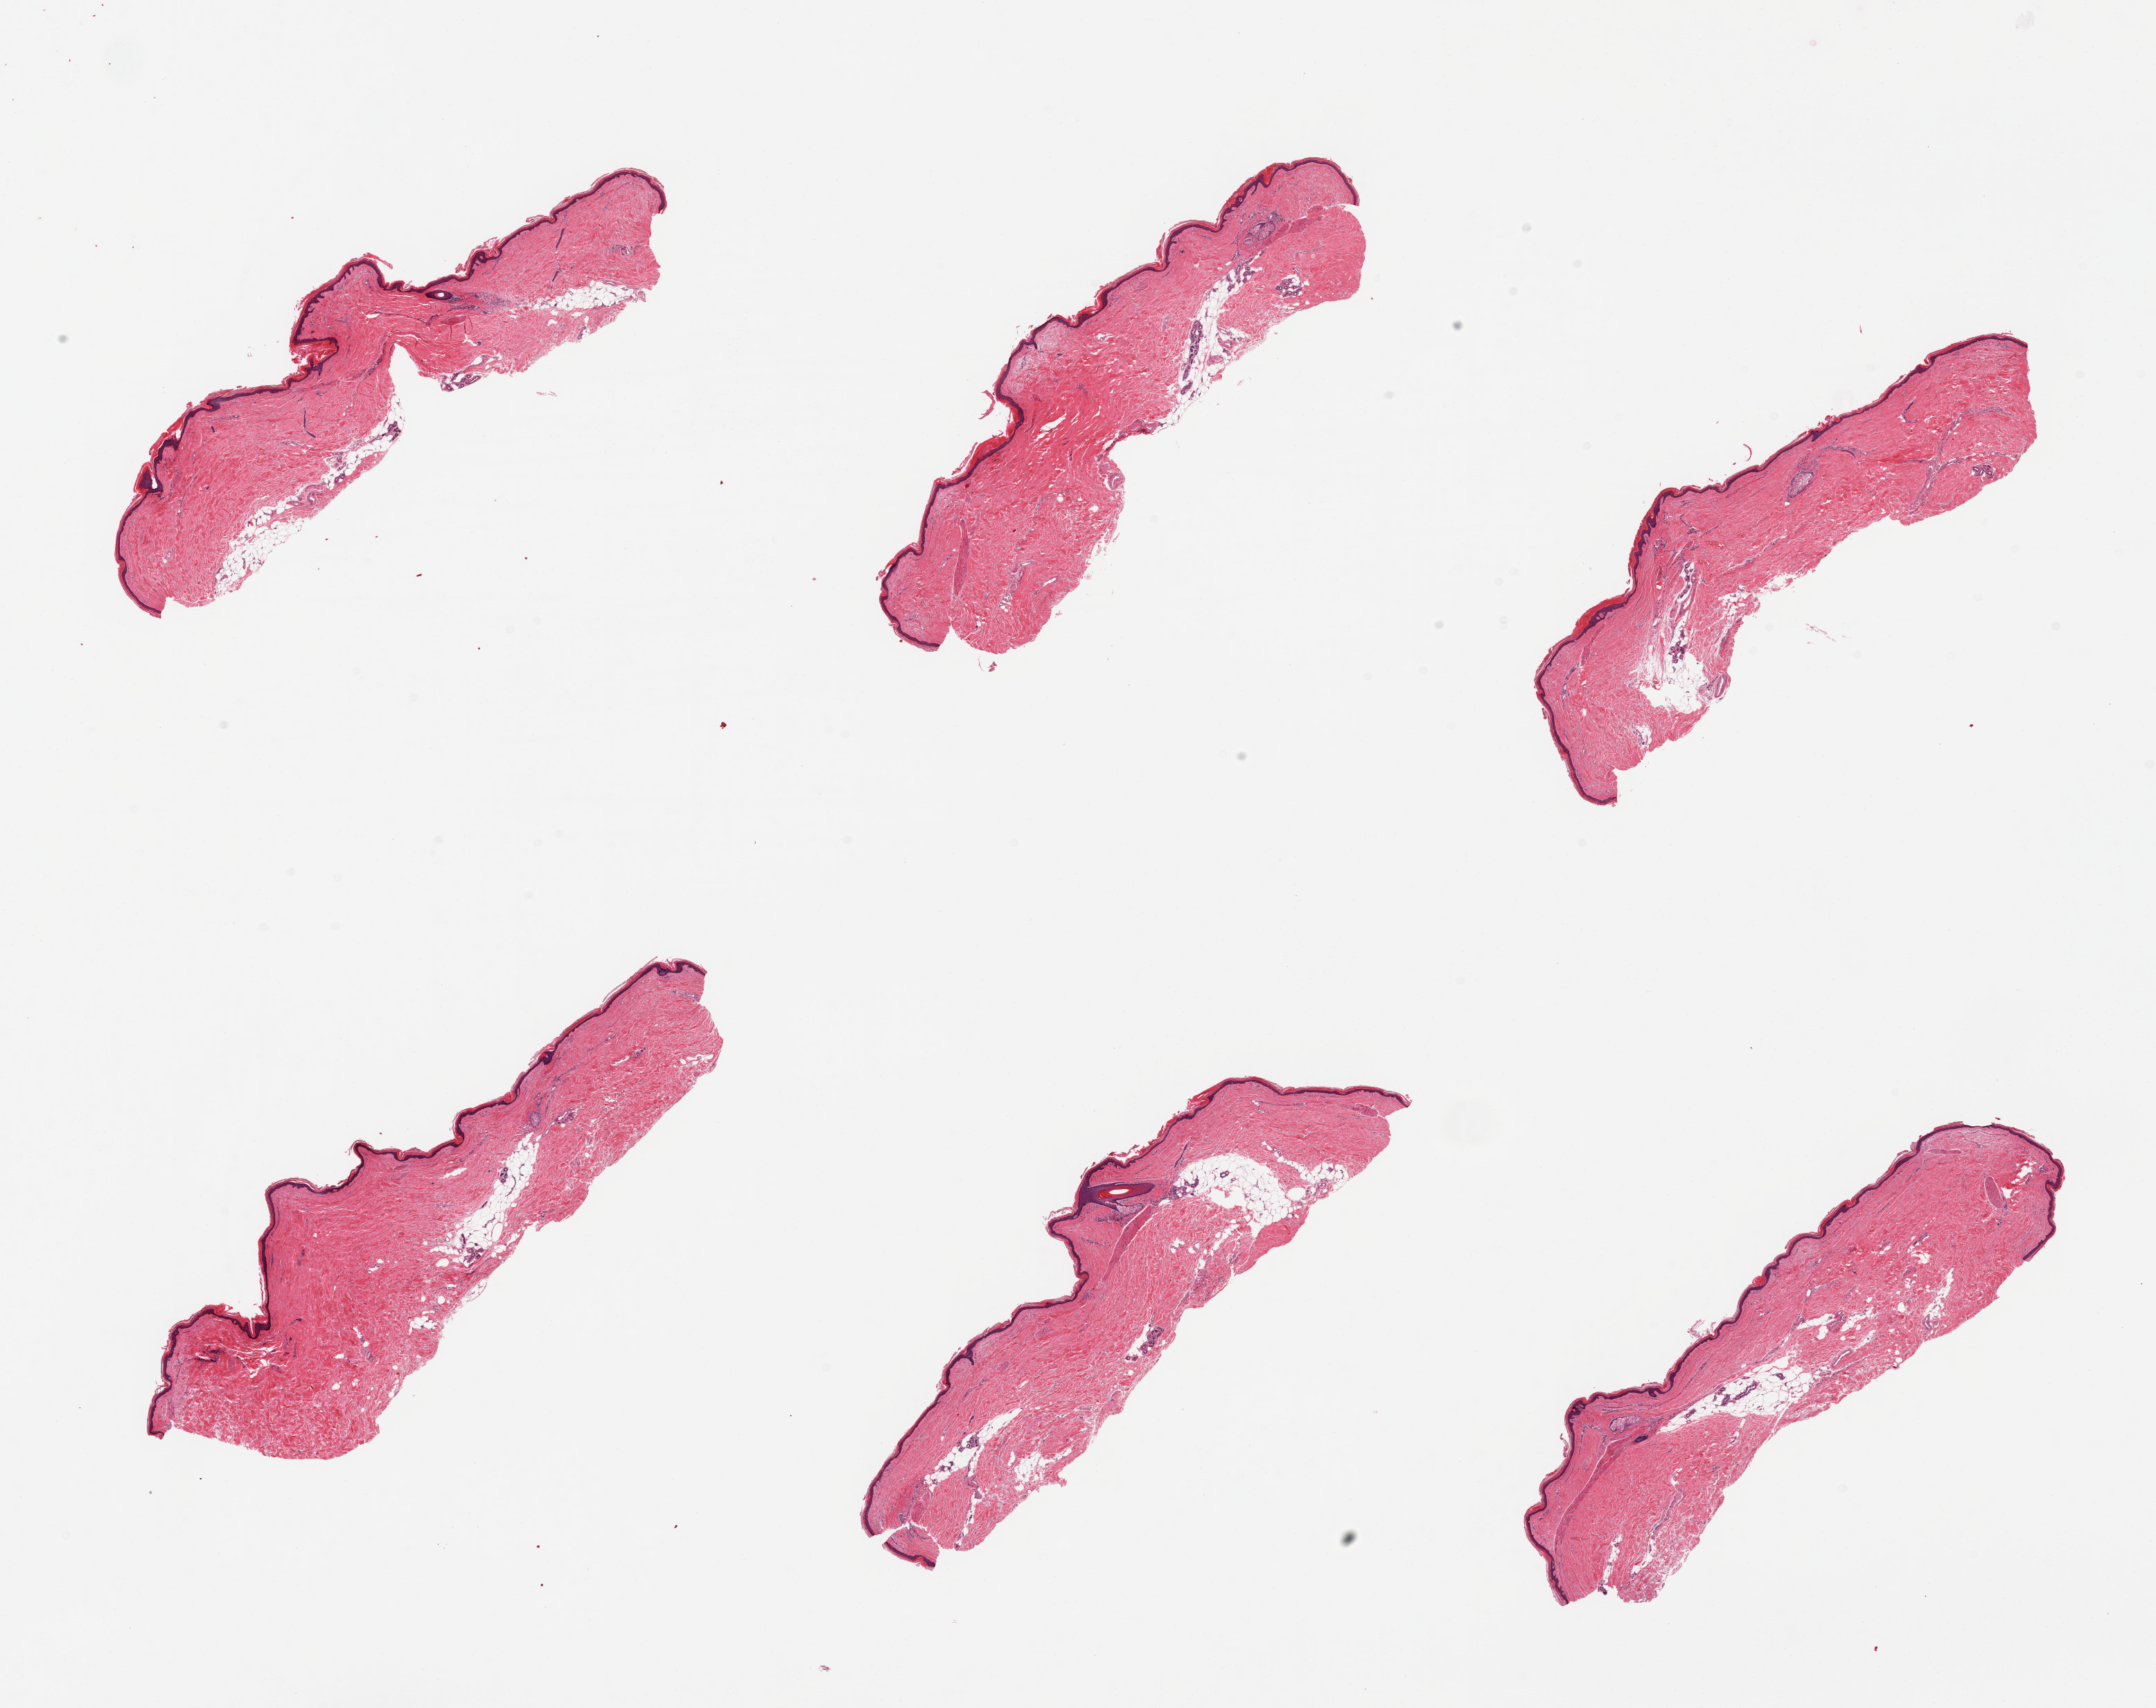
Whole-slide image, haematoxylin and eosin stain — shown as a low-resolution overview of the whole scanned area (about 24.6 x 19.5 mm, from a 20x scan); PAXgene-fixed, paraffin-embedded tissue; target tissue: skin of lower leg; tissue donor sample.
Pathologist's review note for this sample: 6 pieces; well trimmed; 10% intradermal fat.